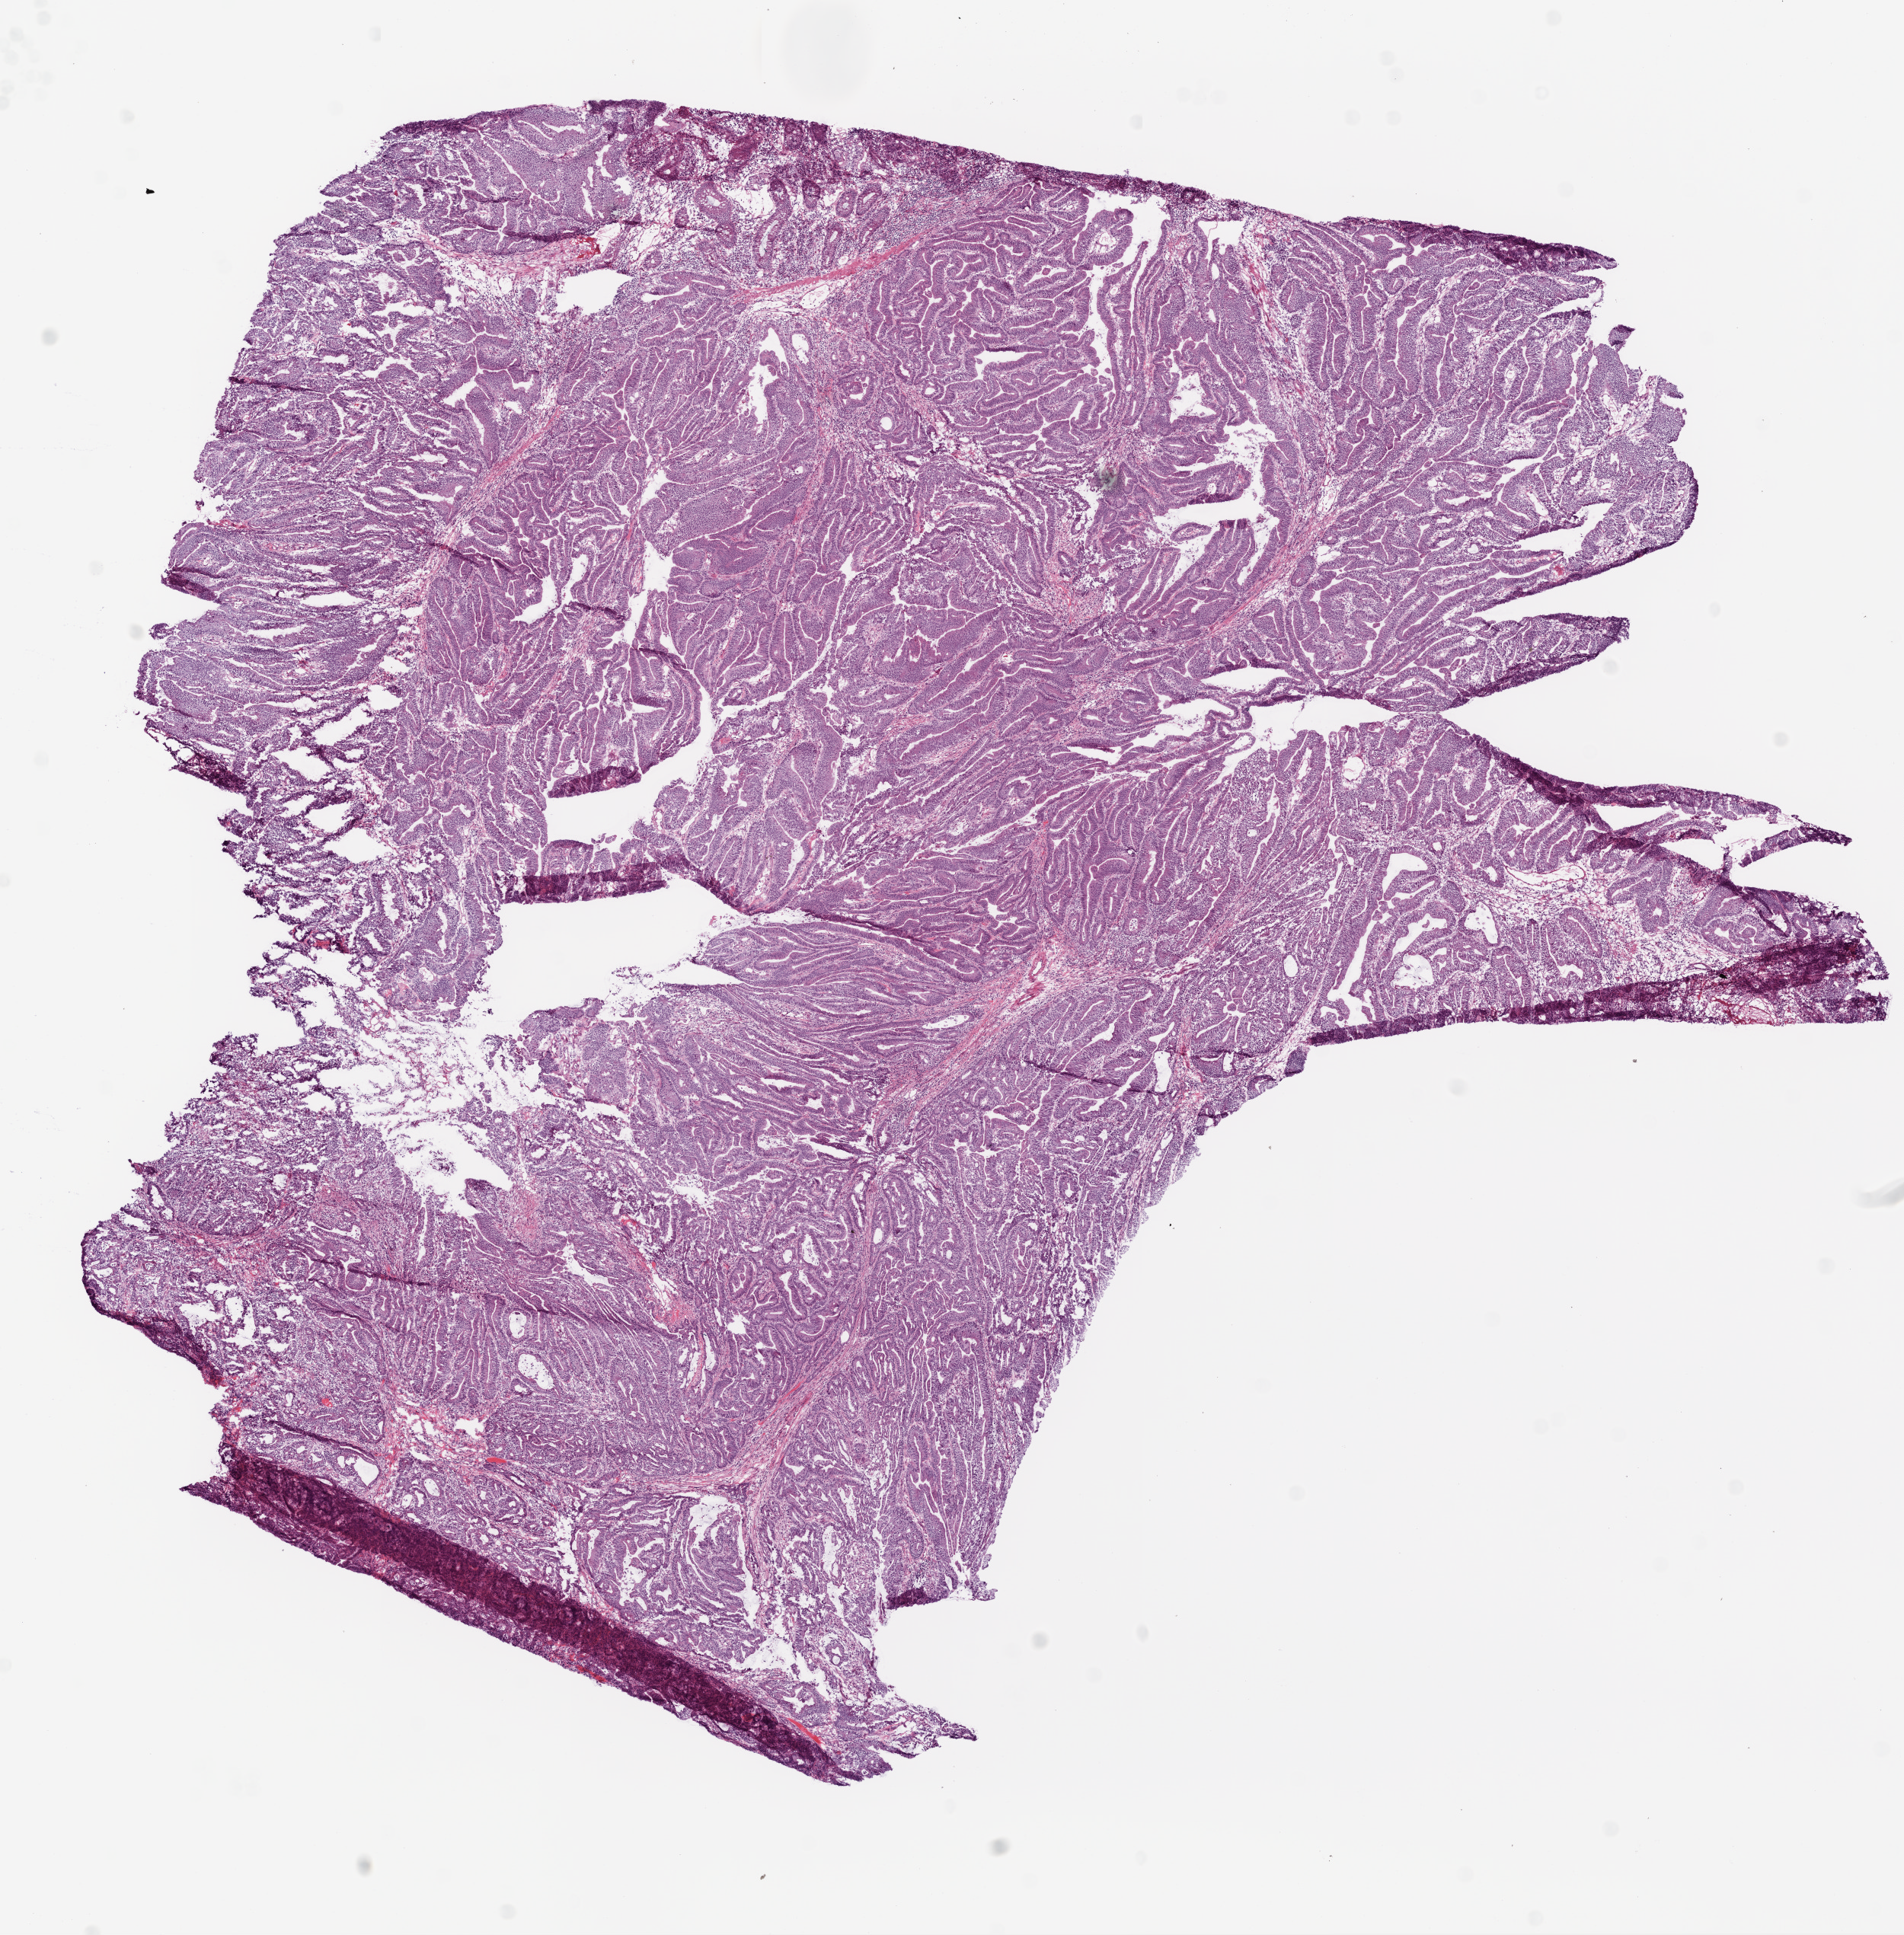
Whole-slide histology image, Hematoxylin and eosin (H&E) stained, low-resolution overview of the scanned area, about 10.0 x 10.2 mm. Frozen section. Primary tumour sample from the colon. Patient: female, age at initial diagnosis 81 years. Pathologist review of this section (percent, as recorded): tumour cells 90%, tumour nuclei 95%, normal cells 0%, stromal cells 10%, necrosis 0%.
* AJCC pathologic stage: IIA (6th edition)
* pathologic diagnosis: Adenocarcinoma, NOS
* TNM: T3 N0 M0
* lymph nodes positive (case pathology): 0 of 27 examined